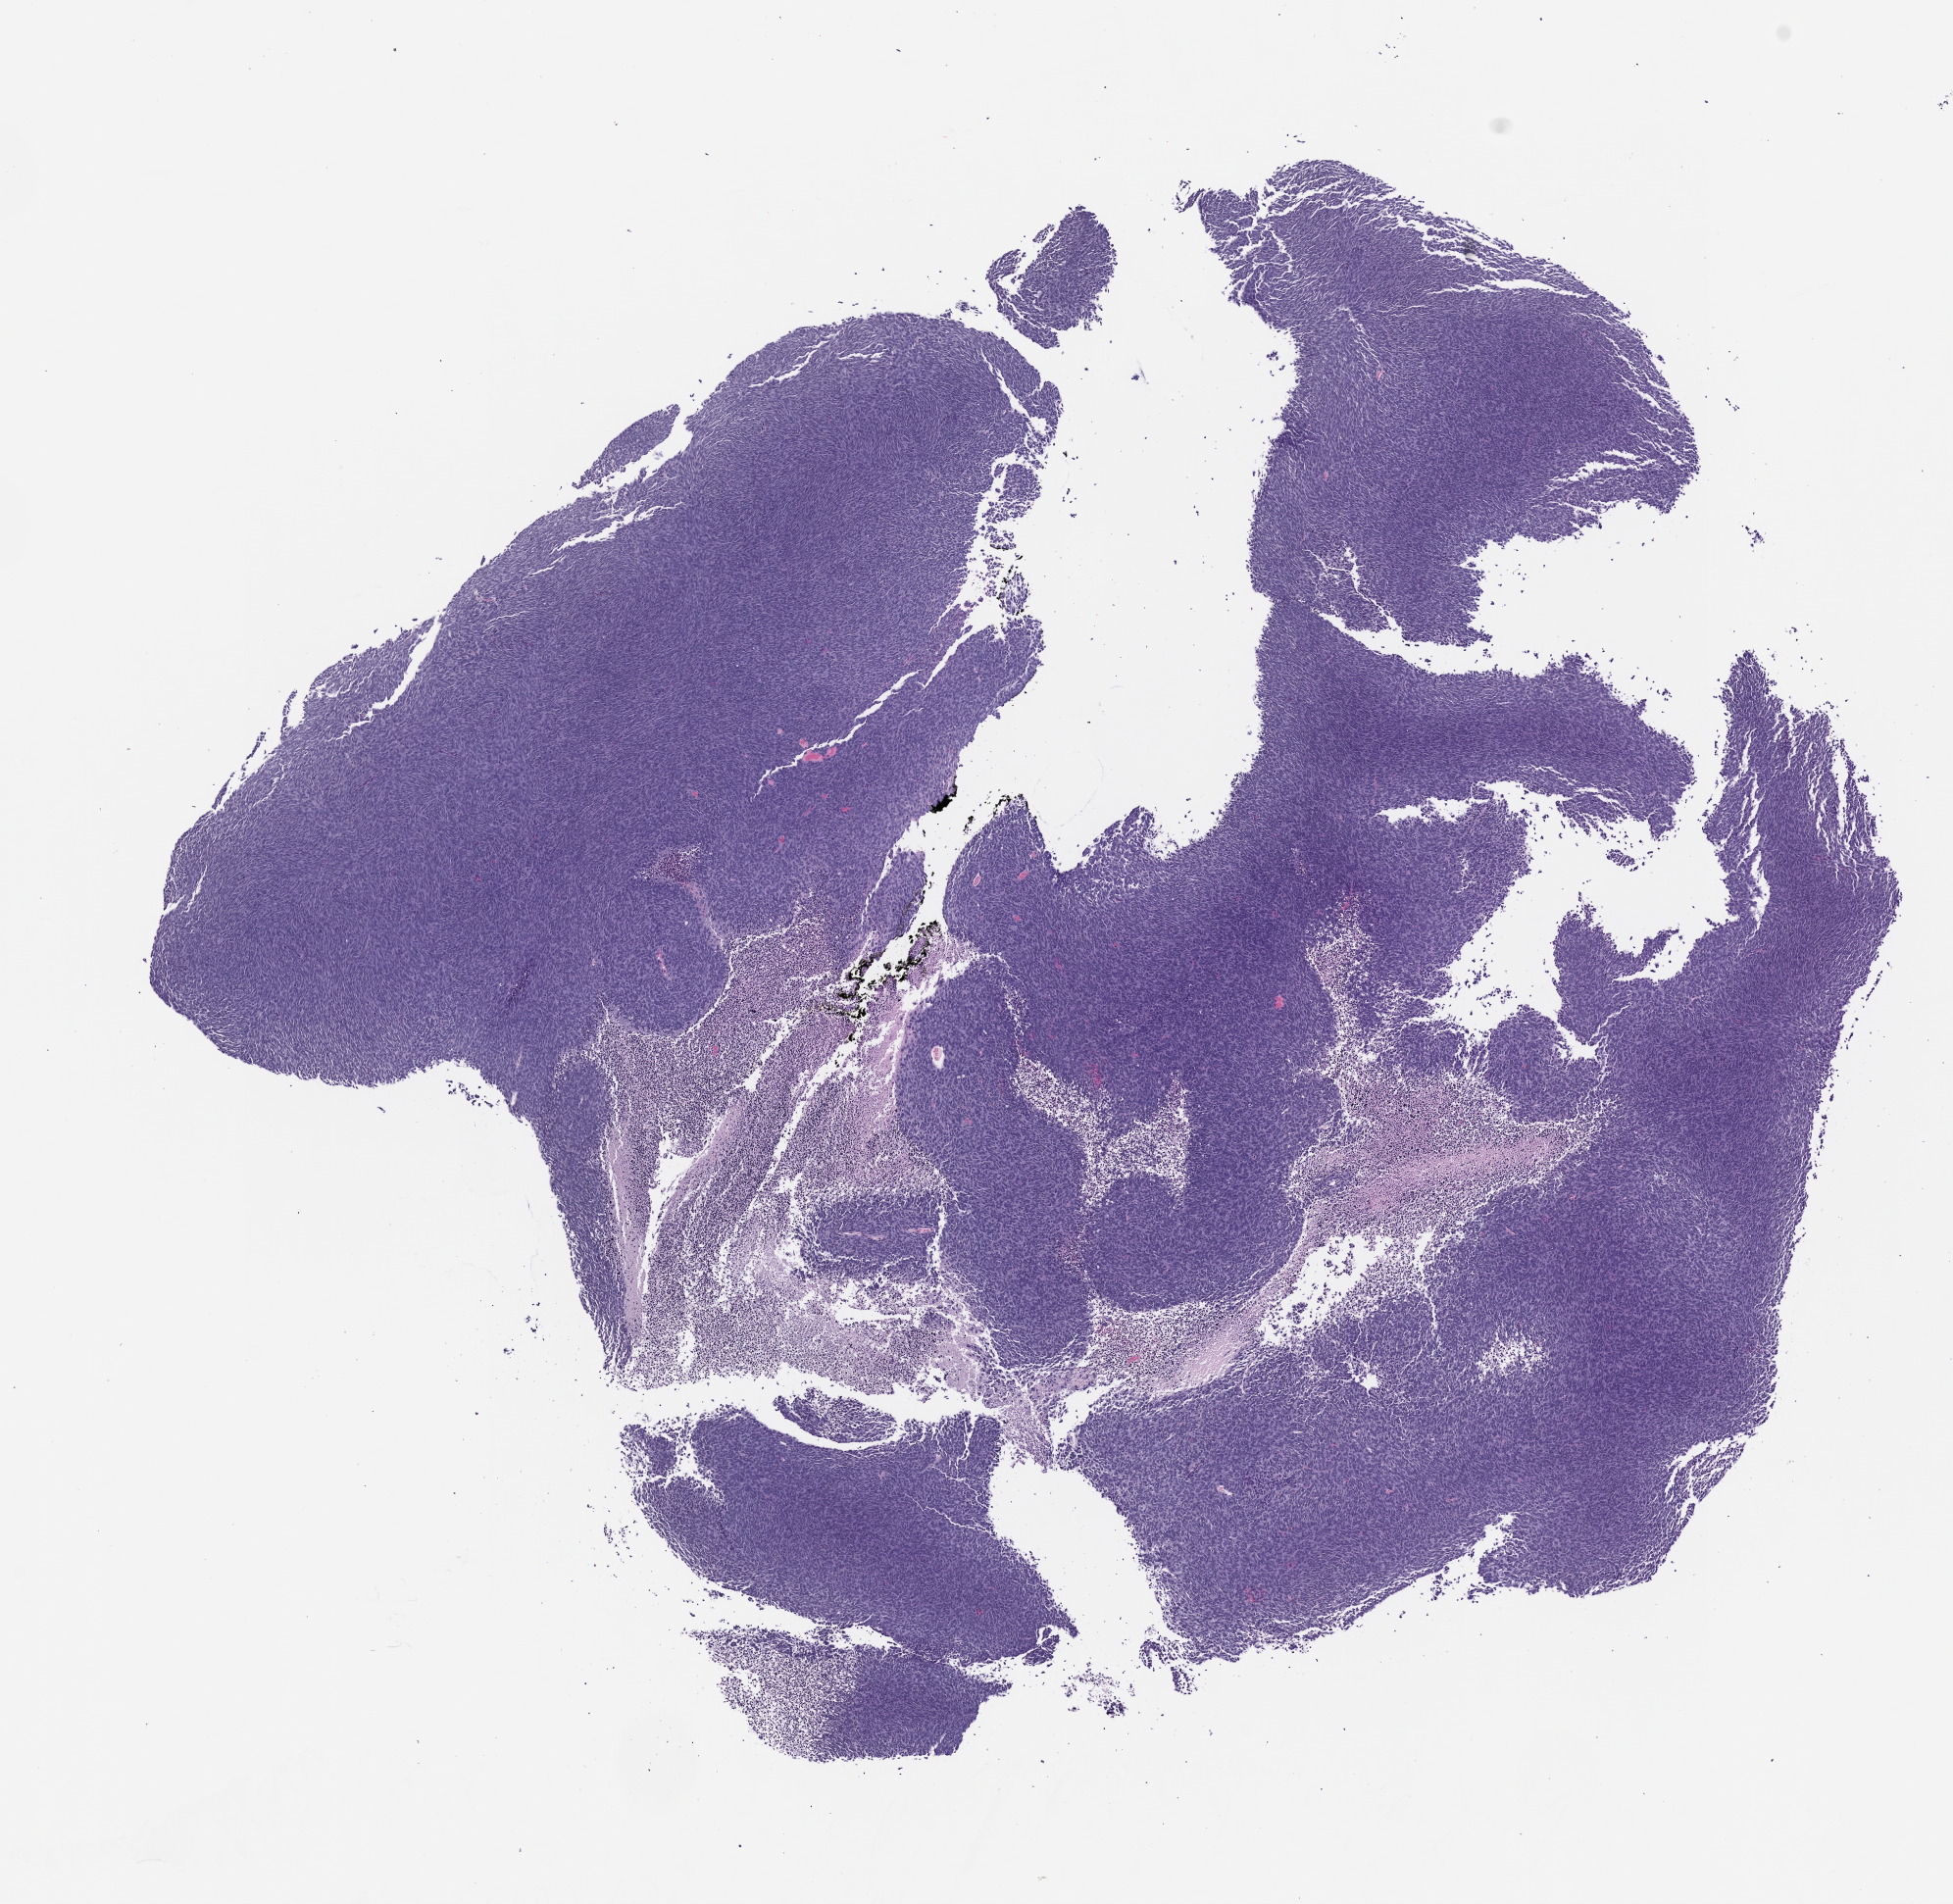
Whole-slide image, hematoxylin and eosin (H&E): patient-derived xenograft (human tumor grown in a mouse), passage 3, a low-resolution overview of the entire scanned area, about 8.0 x 7.8 mm. FFPE section. Originating tumor site category: musculoskeletal.
- originating patient diagnosis: Synovial Sarcoma